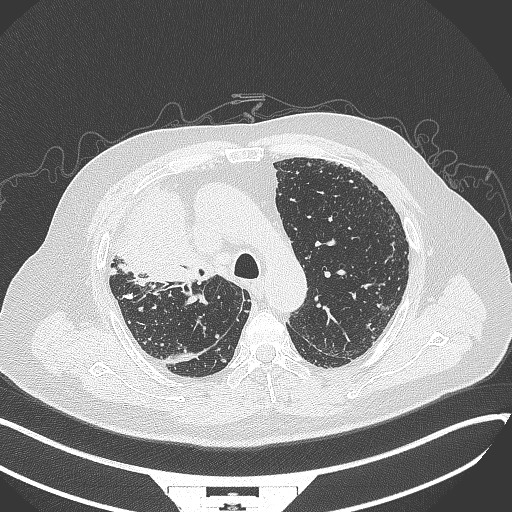
Chest CT, one axial slice. Slice 253 of 384 in the series (ordered by position). Reconstruction kernel B70f. 120 kVp. Lung window (W 1500 / L -600 HU). 1 mm slice thickness. 512 × 512 image matrix. Male patient, age 69 years. From the clinical record (not read from this slice): clinical TNM (as recorded): T4 N3 M1.
Structures marked on this image (bounding box drawn by a radiologist):
- lung tumour (recorded histology: adenocarcinoma): bounding box (x1, y1, x2, y2) in pixels: (115, 186, 208, 286)